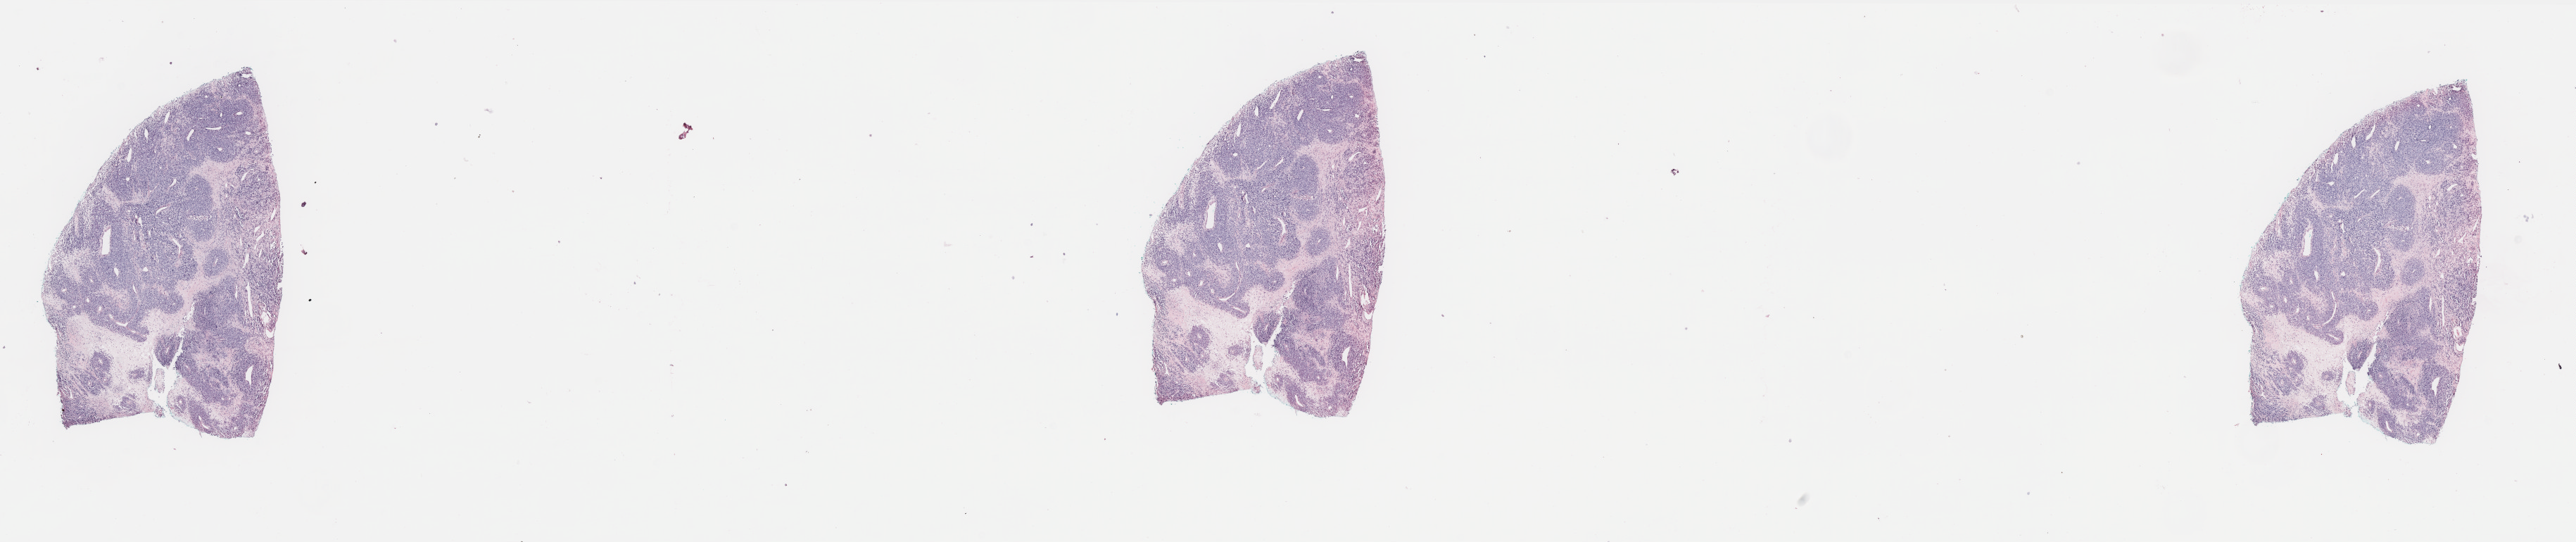
Digitized Hematoxylin and eosin (H&E) stained tissue section (whole slide) — low-resolution overview of the scanned area, about 29.3 x 6.2 mm, formalin-fixed paraffin-embedded (FFPE) diagnostic section, primary tumour sample from the skin. Male, age 62 years at initial diagnosis.
Pathologic diagnosis: Malignant melanoma, NOS.